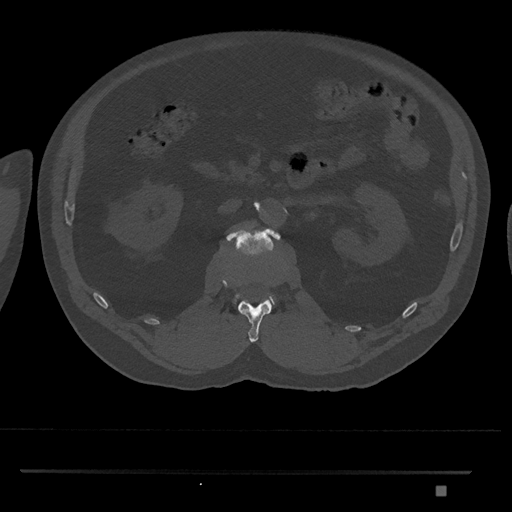
CT including the spine, one axial slice; position 795 of 1134 along the scan axis; 120 kVp; bone window (W 1800 / L 400 HU); 0.5 mm slice thickness; 512 × 512 image matrix, field of view 429 × 429 mm. Patient: male, 65 years. Case-level facts recorded for this patient, not image findings: primary cancer: prostate.
Annotated regions visible in this slice (semi-automatic segmentation, software-assisted and operator-edited):
- L1 vertebra: bounding box [x1, y1, x2, y2] px = [238, 299, 272, 343]
- L2 vertebra: [226, 228, 281, 305]